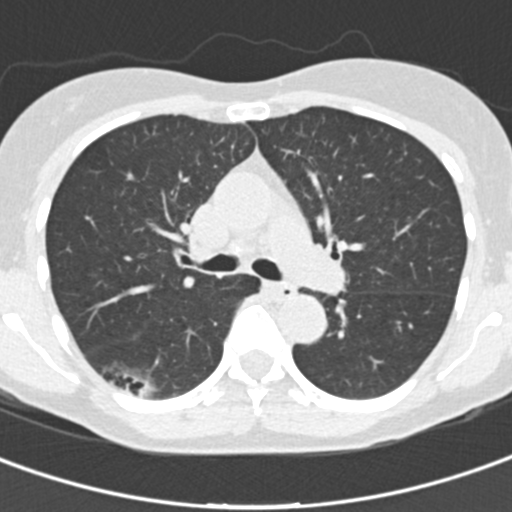
Low-dose screening chest CT, axial slice. First (baseline) screen. Lung window (W 1500 / L -600 HU). Standard (soft-tissue) reconstruction kernel (B30f). 120 kVp. Slice 65 of 162 in the series. 512 × 512 image matrix. Female participant, aged 64 years at enrolment.
Expert reader's lesion annotation, box from (x=84, y=348) to (x=176, y=415) px. The exam's reader record, not a measurement of the box and not confirmed to be the same lesion: non-calcified nodule or mass ≥4 mm, right lower lobe, 31 × 15 mm, poorly defined margins, ground glass attenuation.